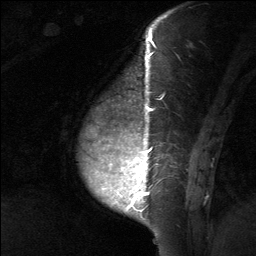
Breast MRI (dynamic contrast-enhanced), one sagittal slice. Position 15 of 64 along the scan axis. Dynamic contrast-enhanced study with each time point stored as its own series, time point 2 of 3 at this slice position (early post-contrast, ordered by acquisition time). 1.5 T. TE 4.8 ms, TR 27 ms. 2 mm slice thickness. 256 × 256 image matrix. Female patient, age 39 years. Case-level facts recorded for this patient, not image findings: setting: breast cancer imaged before/during neoadjuvant chemotherapy; receptor status: HER2-positive.
Outlined on this slice (semi-automatic segmentation, software-assisted and operator-edited):
- analysis volume of interest (the breast-tissue region the enhancement analysis was run in; not a lesion): box from (x=76, y=40) to (x=201, y=217) px
- tumour enhancement mask (voxels above the 90 % enhancement threshold inside the analysis volume of interest): (x=109, y=40)–(x=157, y=208)